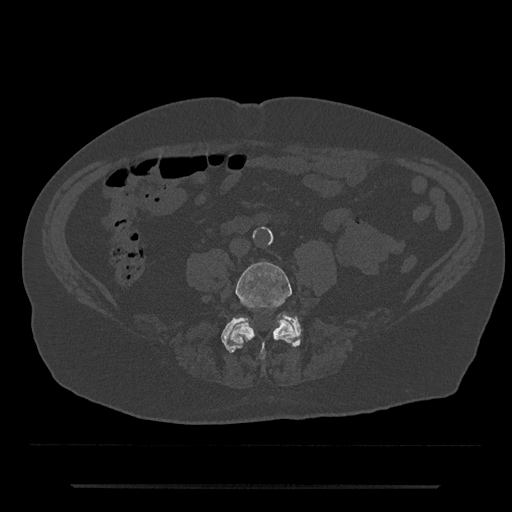
CT including the spine, one axial slice; position 331 of 797 along the scan axis; reconstruction kernel Br40s/3; bone window (W 1800 / L 400 HU); 0.5 mm slice thickness; 512 × 512 image matrix, field of view 434 × 434 mm. Patient: male, 80 years. From the clinical record (not read from this slice): primary cancer: prostate; vertebrae with lytic lesions (as recorded): L1, T11.
Outlined on this slice (semi-automatic segmentation, software-assisted and operator-edited):
- L4 vertebra: box from (x=227, y=262) to (x=296, y=359) px
- L5 vertebra: (x=221, y=314)–(x=302, y=353)